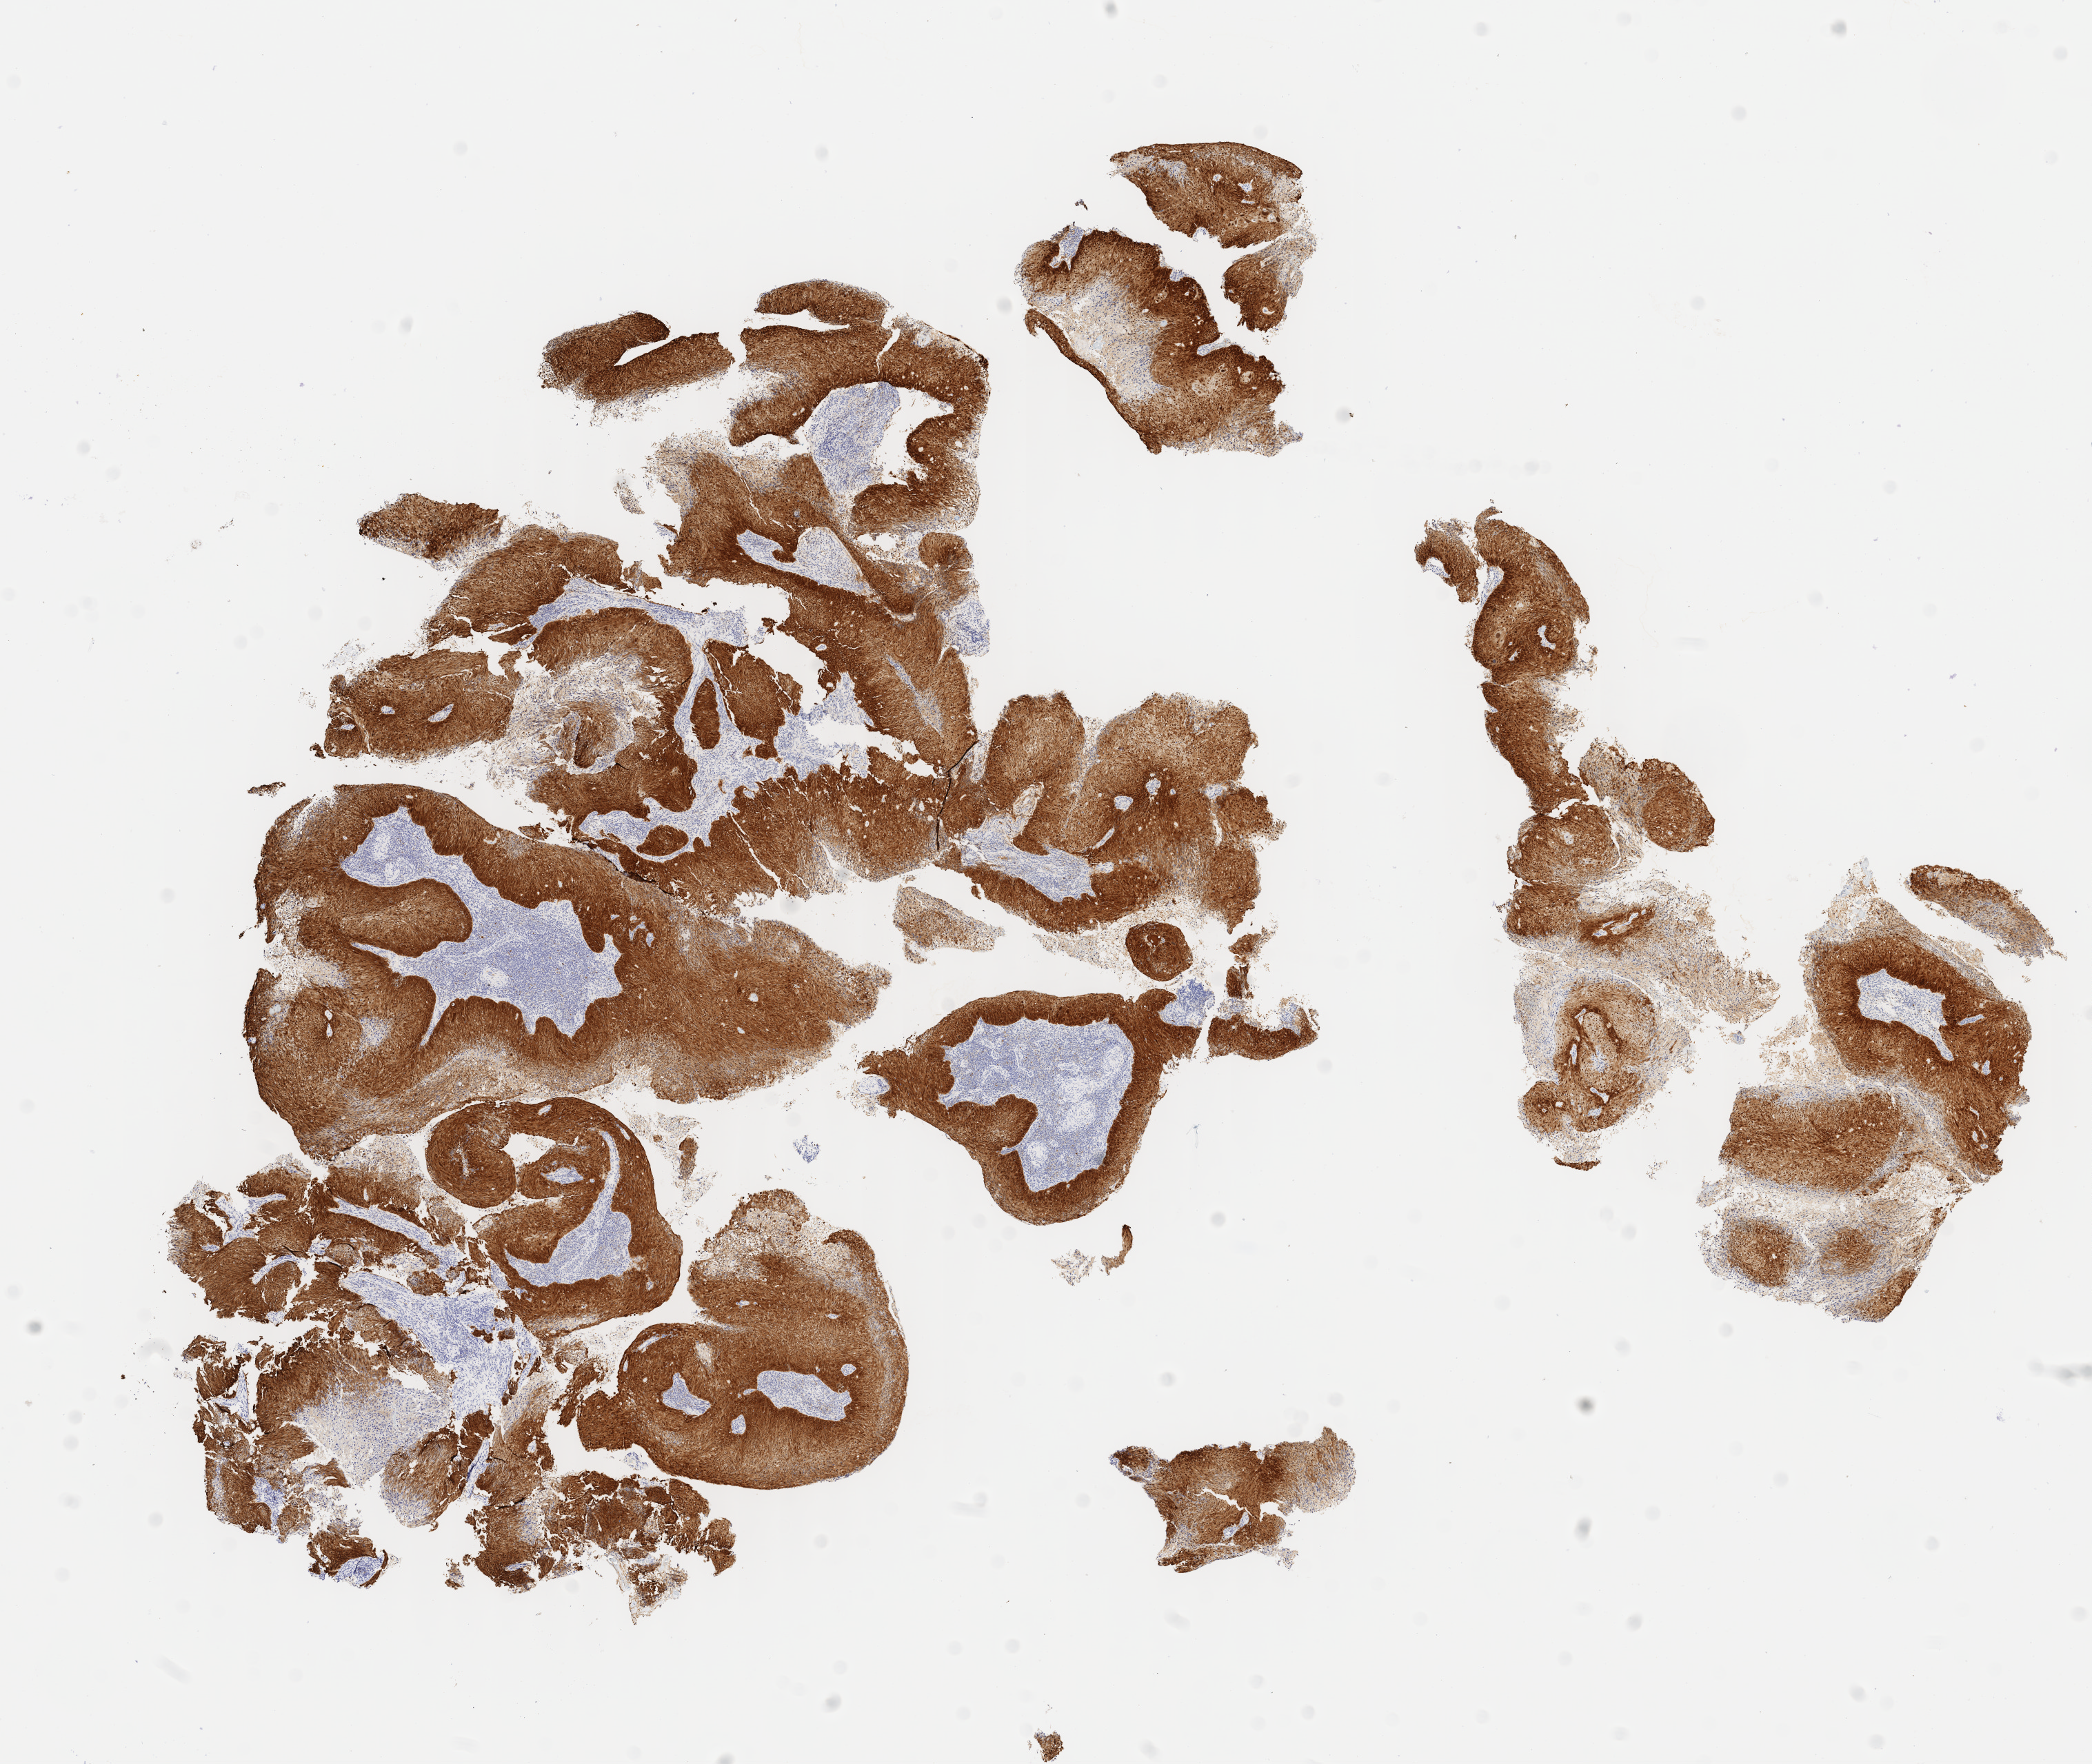
Whole-slide image, immunohistochemical stain for p16 (p16INK4a) — low-resolution overview of the scanned area, about 12.1 x 10.2 mm; specimen: tumor tissue; site: cervix. Patient: female, age 60 years.
• histologic diagnosis: Squamous cell carcinoma, large cell, nonkeratinizing, NOS